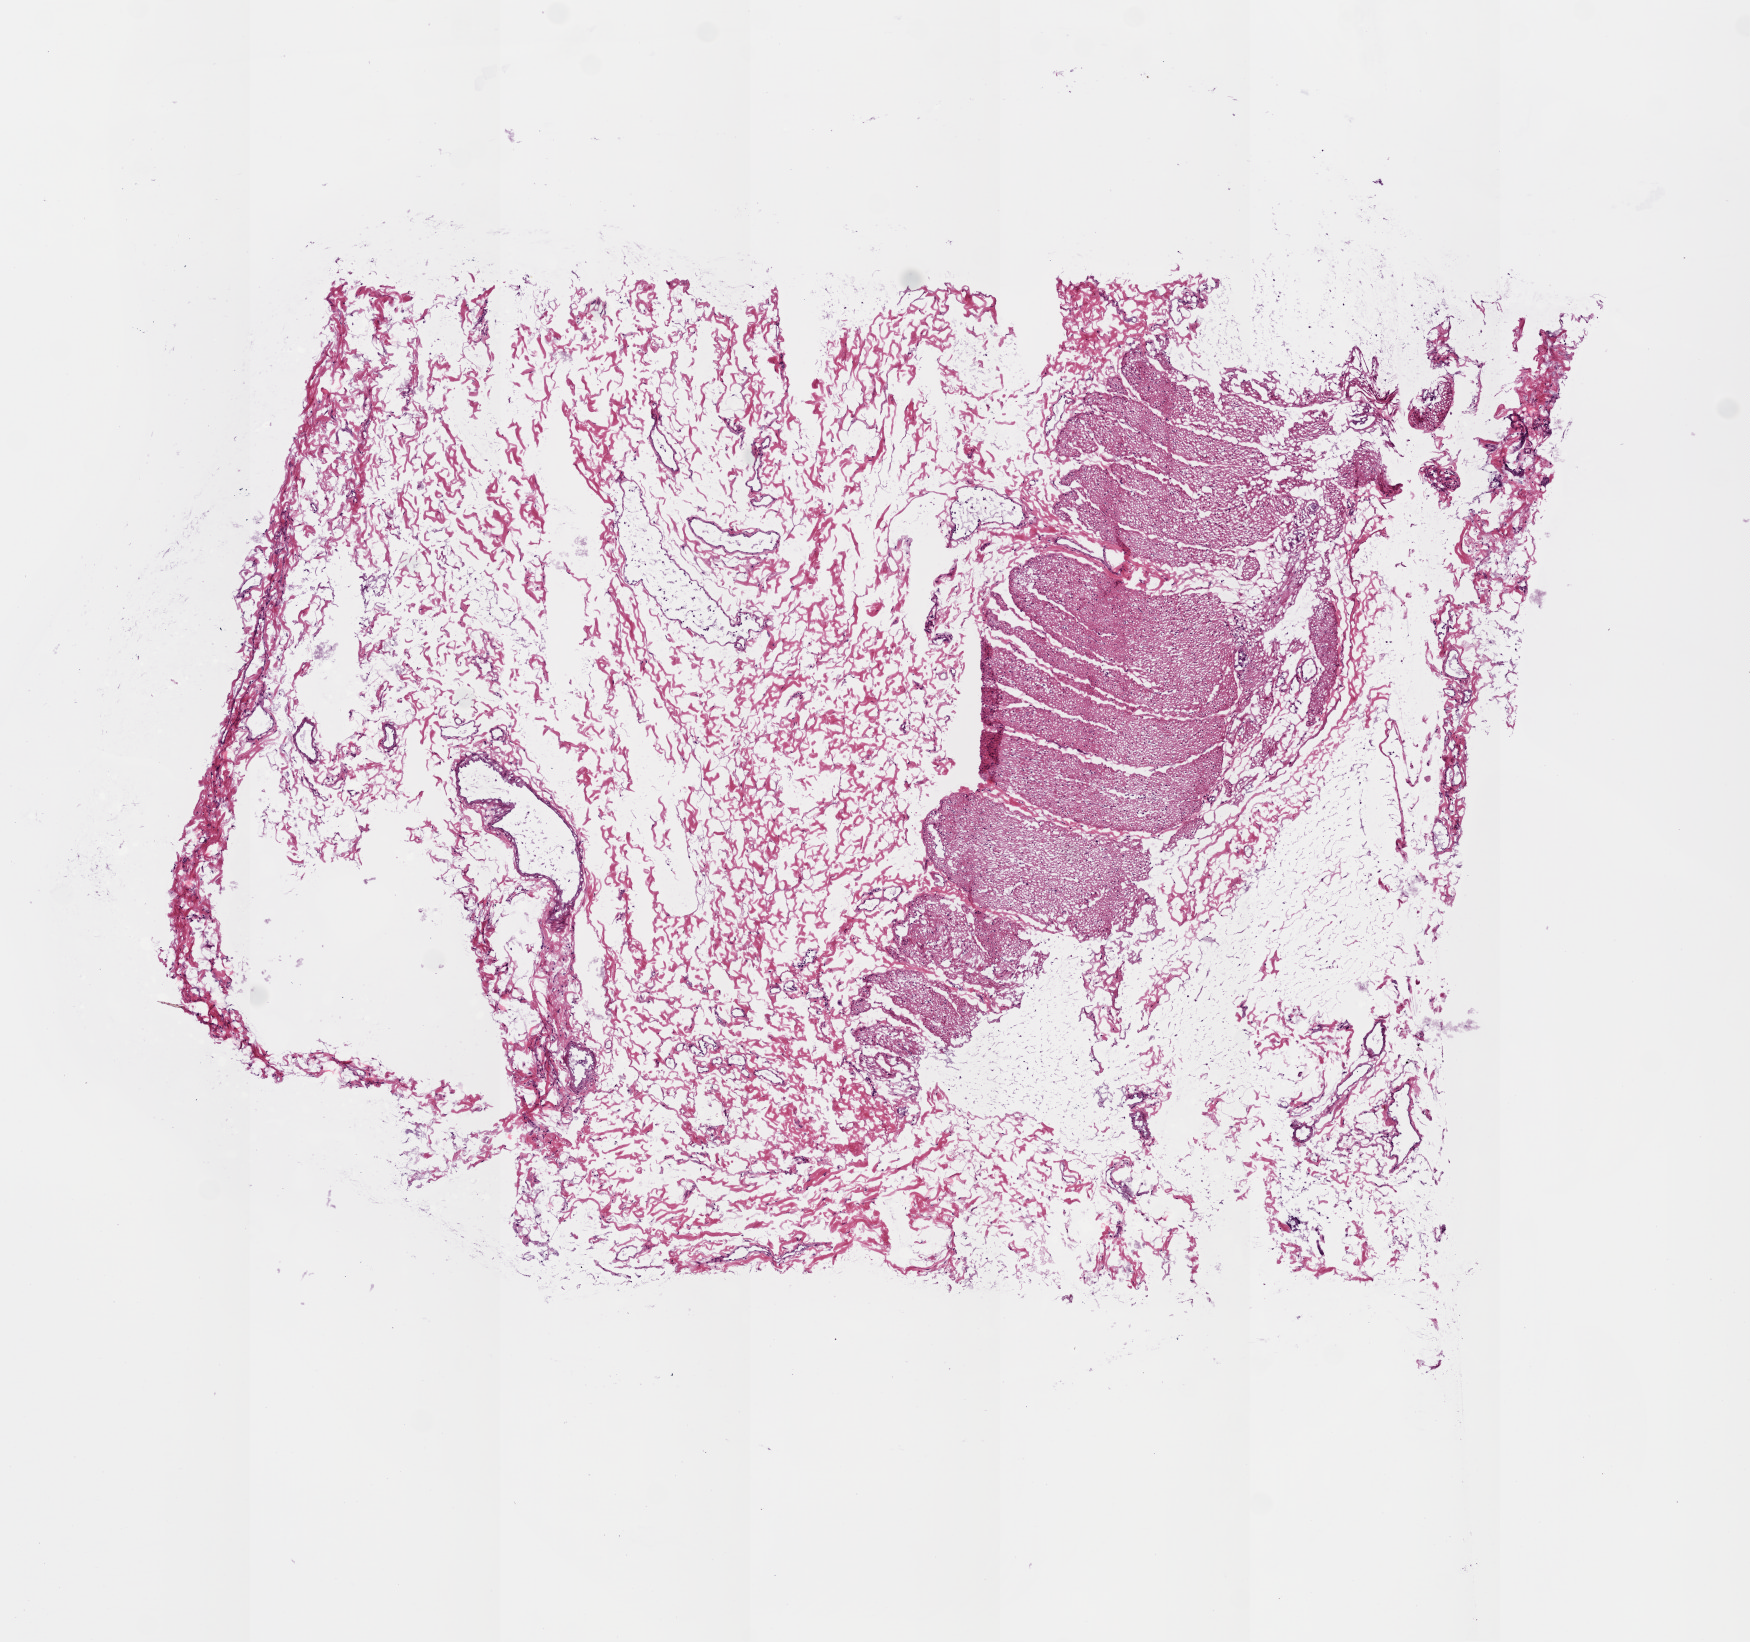
H&E whole-slide image — low-resolution overview of the scanned area, about 7.0 x 6.6 mm; frozen section; colon, solid tissue normal (non-tumour tissue) sample. Female patient; age at initial diagnosis 68 years.
This section: solid tissue normal (non-tumour) sample from the same patient. Patient diagnosis: Adenocarcinoma, NOS (ascending colon).